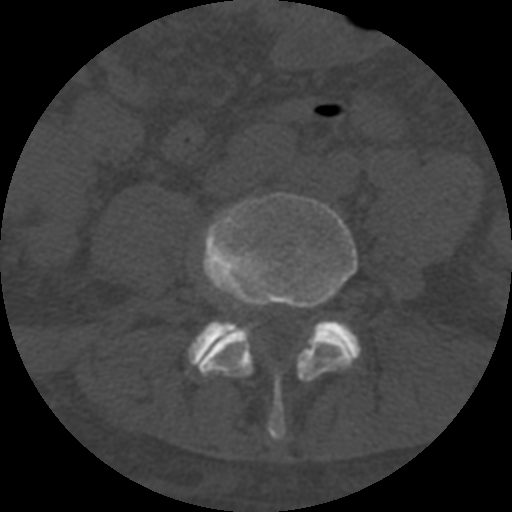
CT including the spine, one axial slice; position 200 of 708 along the scan axis; reconstruction kernel STANDARD; one of 3 acquisitions stored at this slice position; bone window (W 1800 / L 400 HU); 1.25 mm slice thickness; 512 × 512 image matrix. Patient age 55 years. From the clinical record (not read from this slice): primary cancer: colon; vertebrae with lytic lesions (as recorded): T12, L1, L5.
Annotated regions visible in this slice (semi-automatically segmented with operator editing):
- L4 vertebra: bounding box (x1, y1, x2, y2) in pixels: (198, 192, 358, 440)
- L5 vertebra: (187, 320, 361, 368)